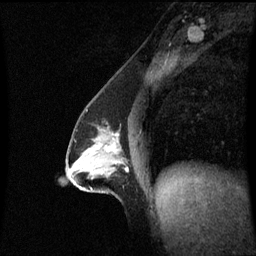
Breast MRI (dynamic contrast-enhanced), one sagittal slice. Position 32 of 60 along the scan axis. Dynamic contrast-enhanced series, image 2 of 3 at this slice position (ordered by acquisition). 1.5 T. TE 4.2 ms, TR 8.9 ms. 2.2 mm slice thickness. 256 × 256 image matrix. Female patient, age 47 years. Case-level facts recorded for this patient, not image findings: setting: breast cancer imaged before/during neoadjuvant chemotherapy; receptor status: HR-positive, HER2-negative.
Structures marked on this image (semi-automatically segmented with operator editing):
- analysis volume of interest (the breast-tissue region the enhancement analysis was run in; not a lesion): bounding box (x1, y1, x2, y2) in pixels: (64, 119, 130, 195)
- tumour enhancement mask (voxels above the 70 % enhancement threshold inside the analysis volume of interest): (99, 139, 118, 163)